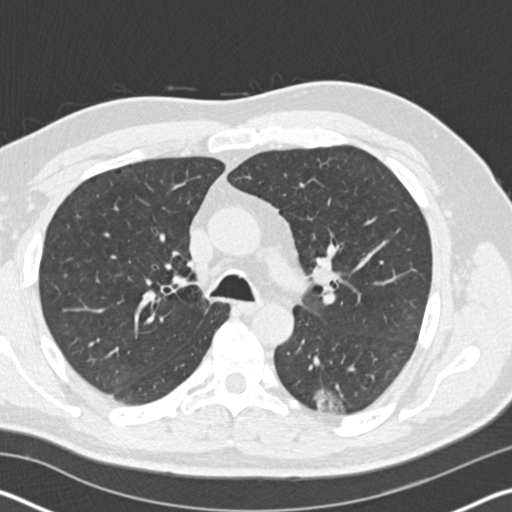
Low-dose screening chest CT, one axial slice; 120 kVp; lung window (W 1500 / L -600 HU); 2 mm slice thickness; 512 × 512 image matrix, field of view 340 × 340 mm.
Outlined on this slice (manually delineated by an expert):
- lesion 1 (tumor, lower lobe of left lung): bounding box <314,389,345,416> (left, top, right, bottom; pixels)